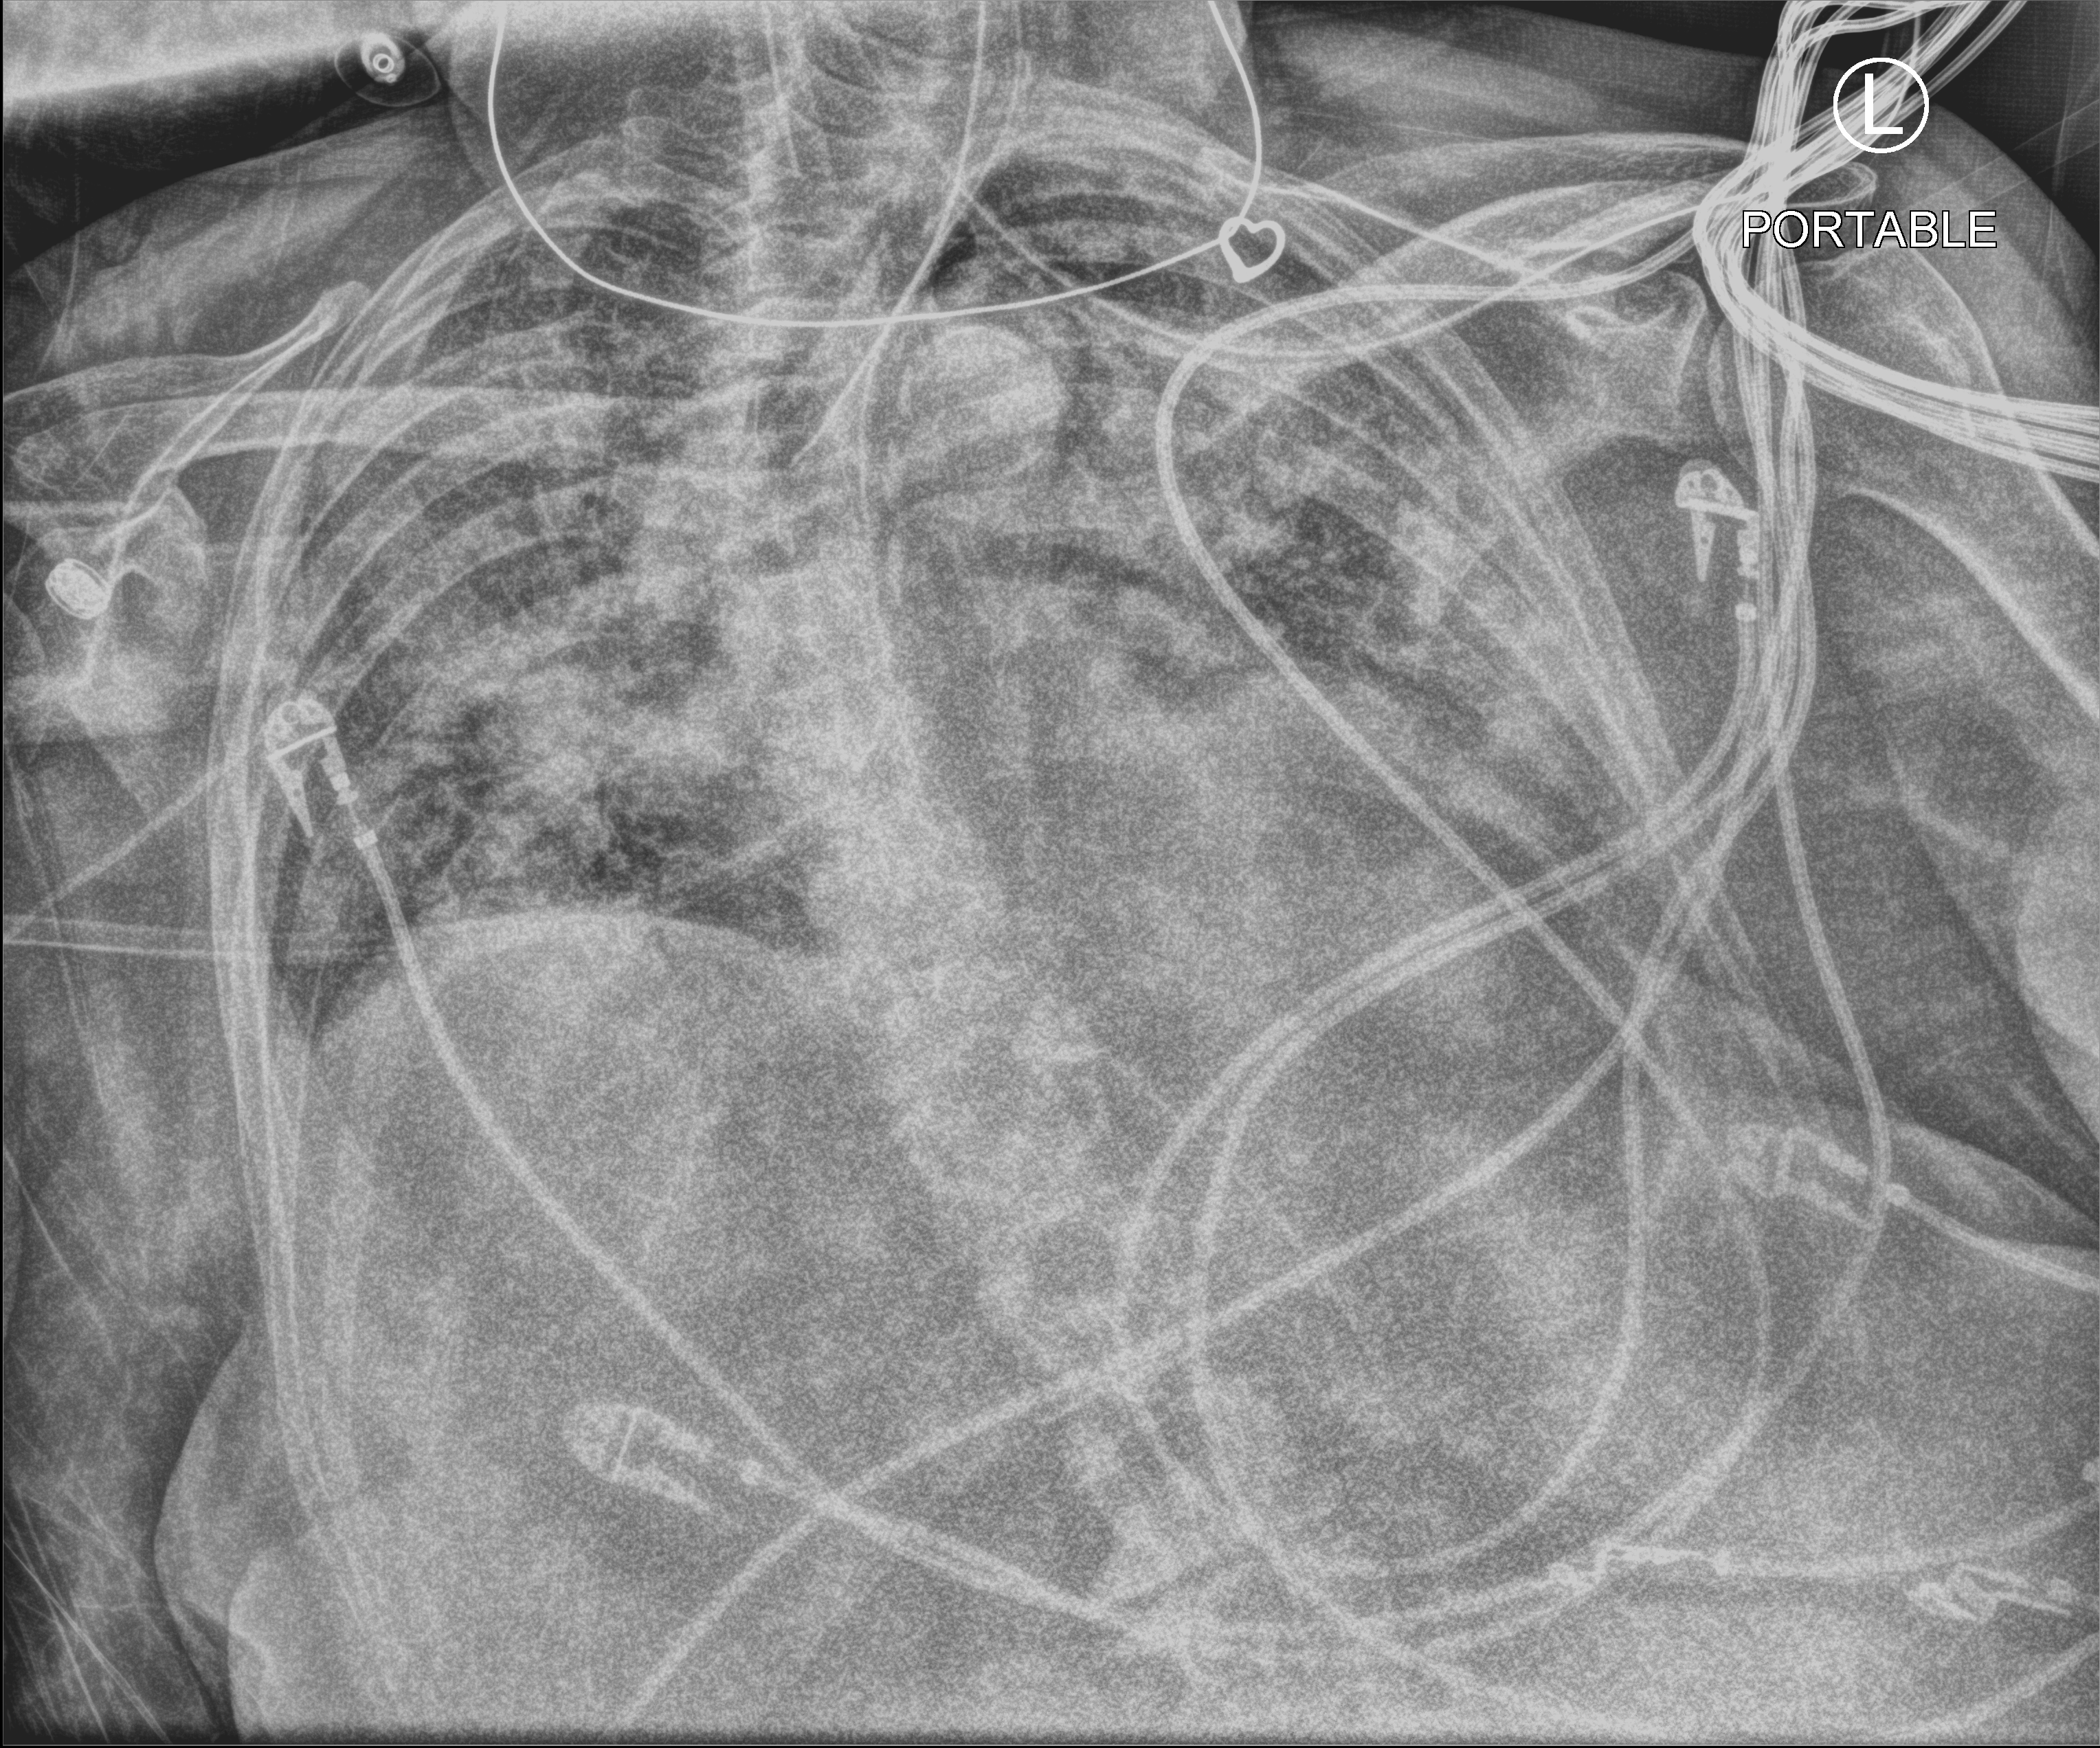
Bedside chest radiograph (computed radiography); anteroposterior (AP) projection. Patient hospitalised with COVID-19; female, aged 75–90 years.
Hospital-stay facts (about this admission, not read from this image; timing relative to this image not recorded): mechanically ventilated during this hospital stay: yes.